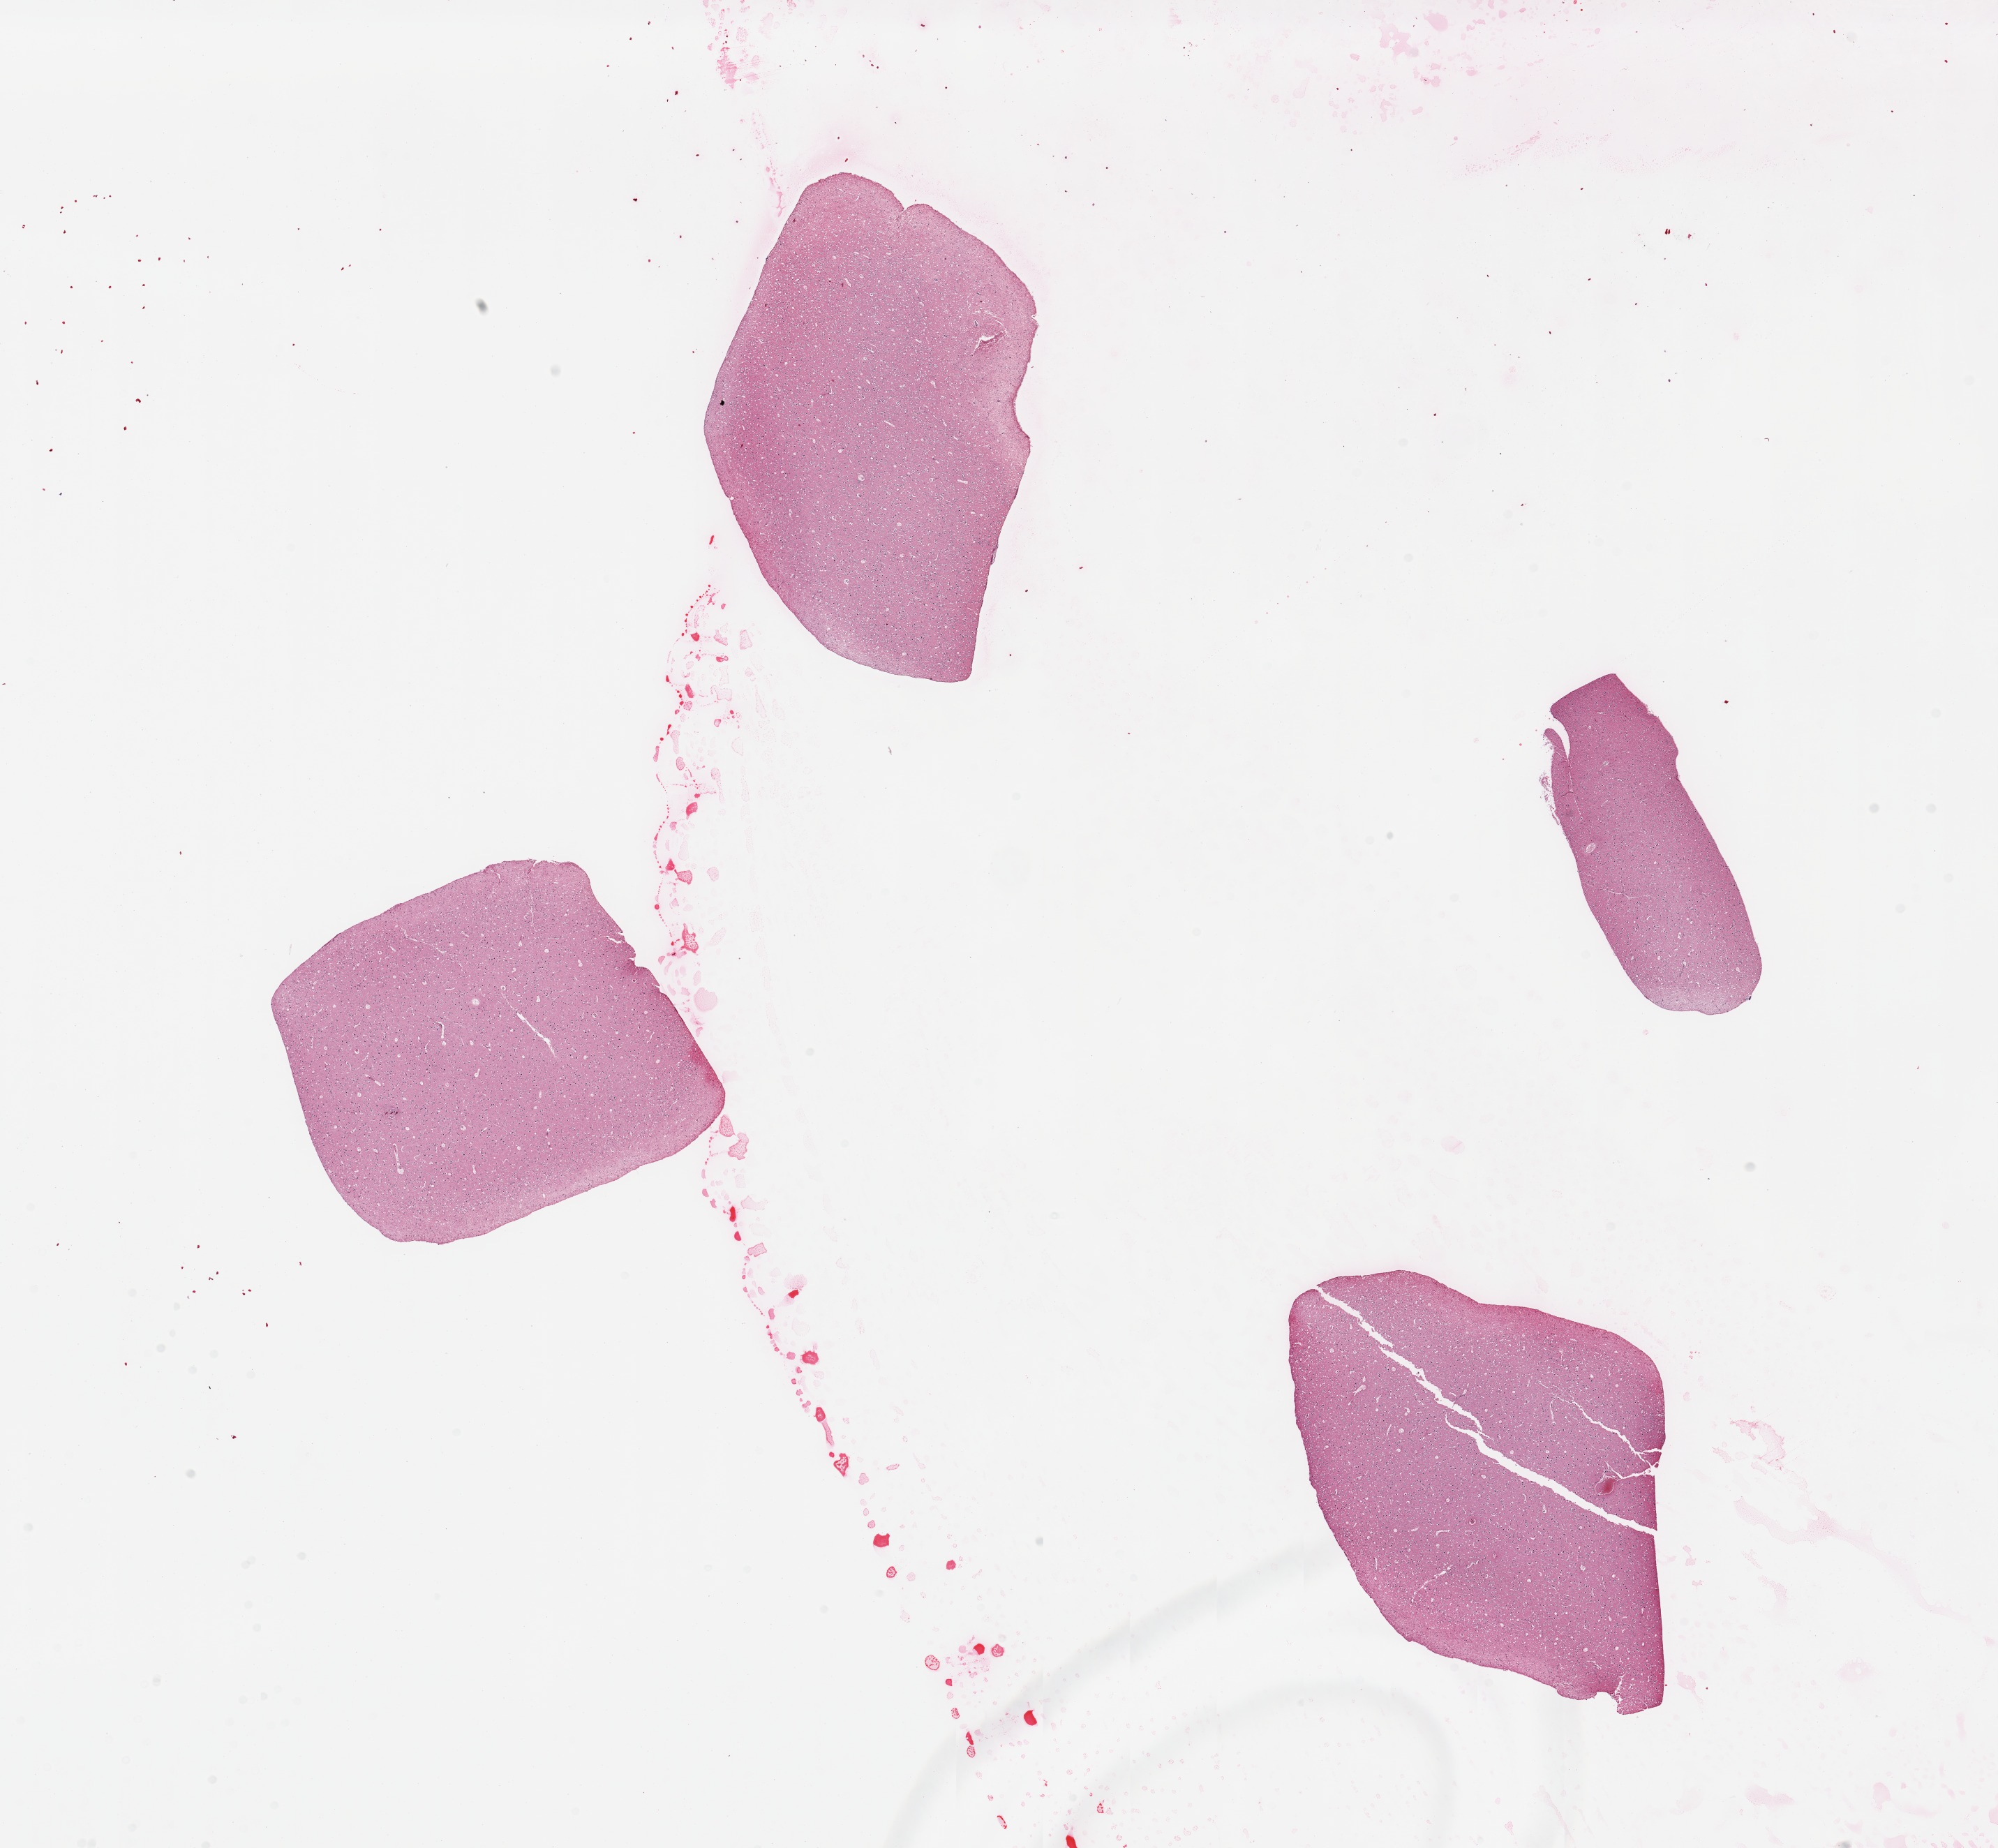
Digitized hematoxylin and eosin (H&E)-stained section, whole scanned area (about 22.6 x 20.9 mm, slide scanned at 20x) shown as a low-resolution overview. PAXgene-fixed paraffin-embedded (PFPE) section. Sampled site (target tissue): cerebral cortex. Tissue donor sample. Donor: male.
Reviewer comment on this tissue sample: 4 pieces.